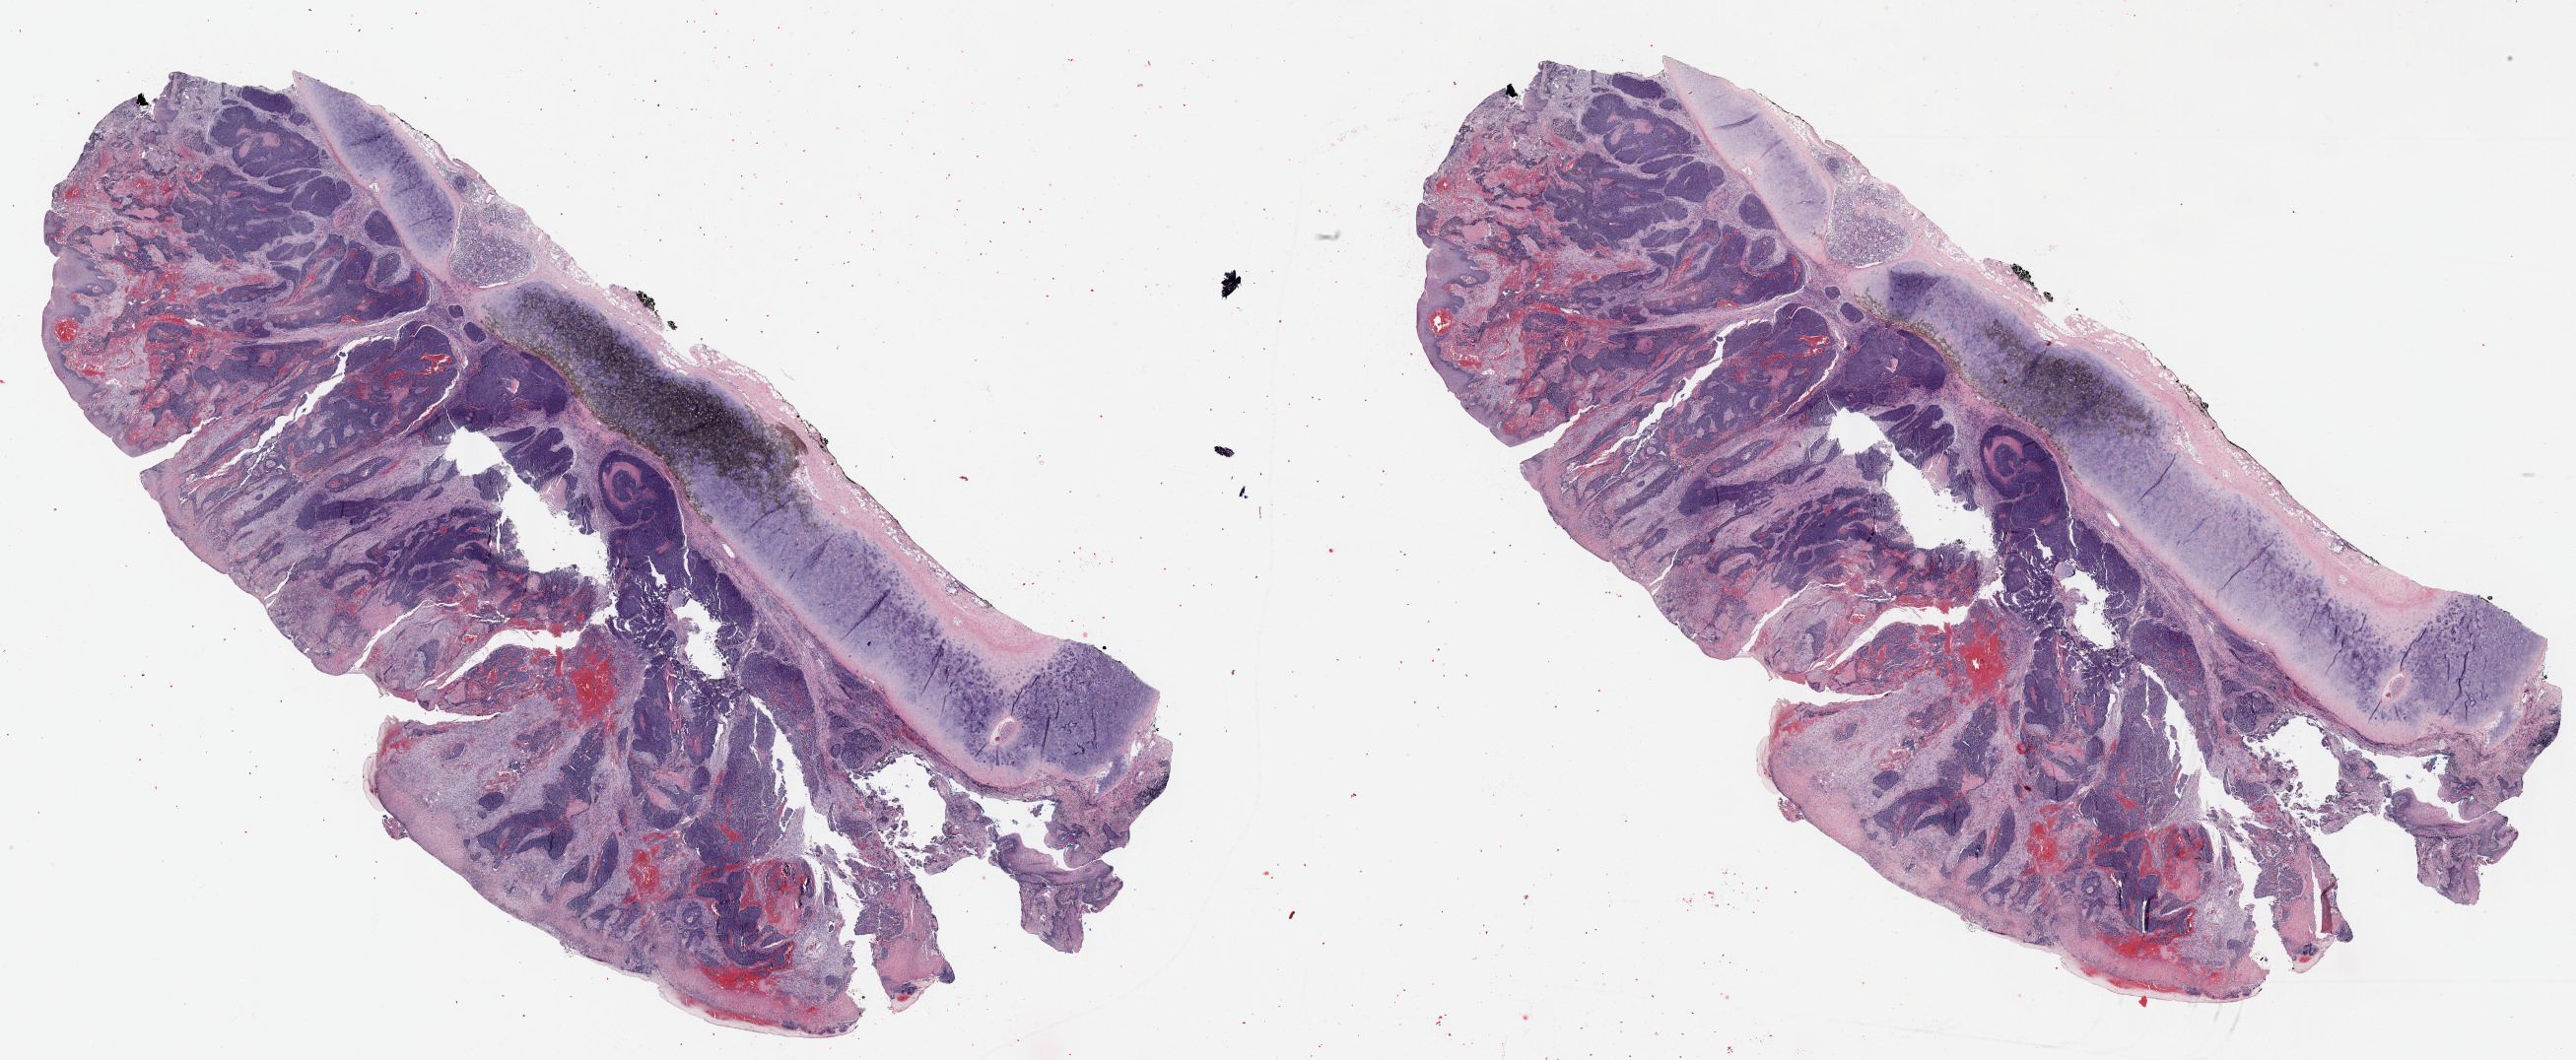
Digitized H&E-stained tissue section (whole slide) — whole scanned area (about 42.3 x 17.4 mm, from a 40x scan) shown as a low-resolution overview, formalin-fixed paraffin-embedded (FFPE) diagnostic section, sample: primary tumour, head and neck. Female, age 69 years at initial diagnosis. Histologic grade: G2 (moderately differentiated).
Lymph nodes positive (case pathology): 1 of 7 examined. AJCC pathologic stage: III. Histologic diagnosis: Basaloid squamous cell carcinoma (larynx, NOS).